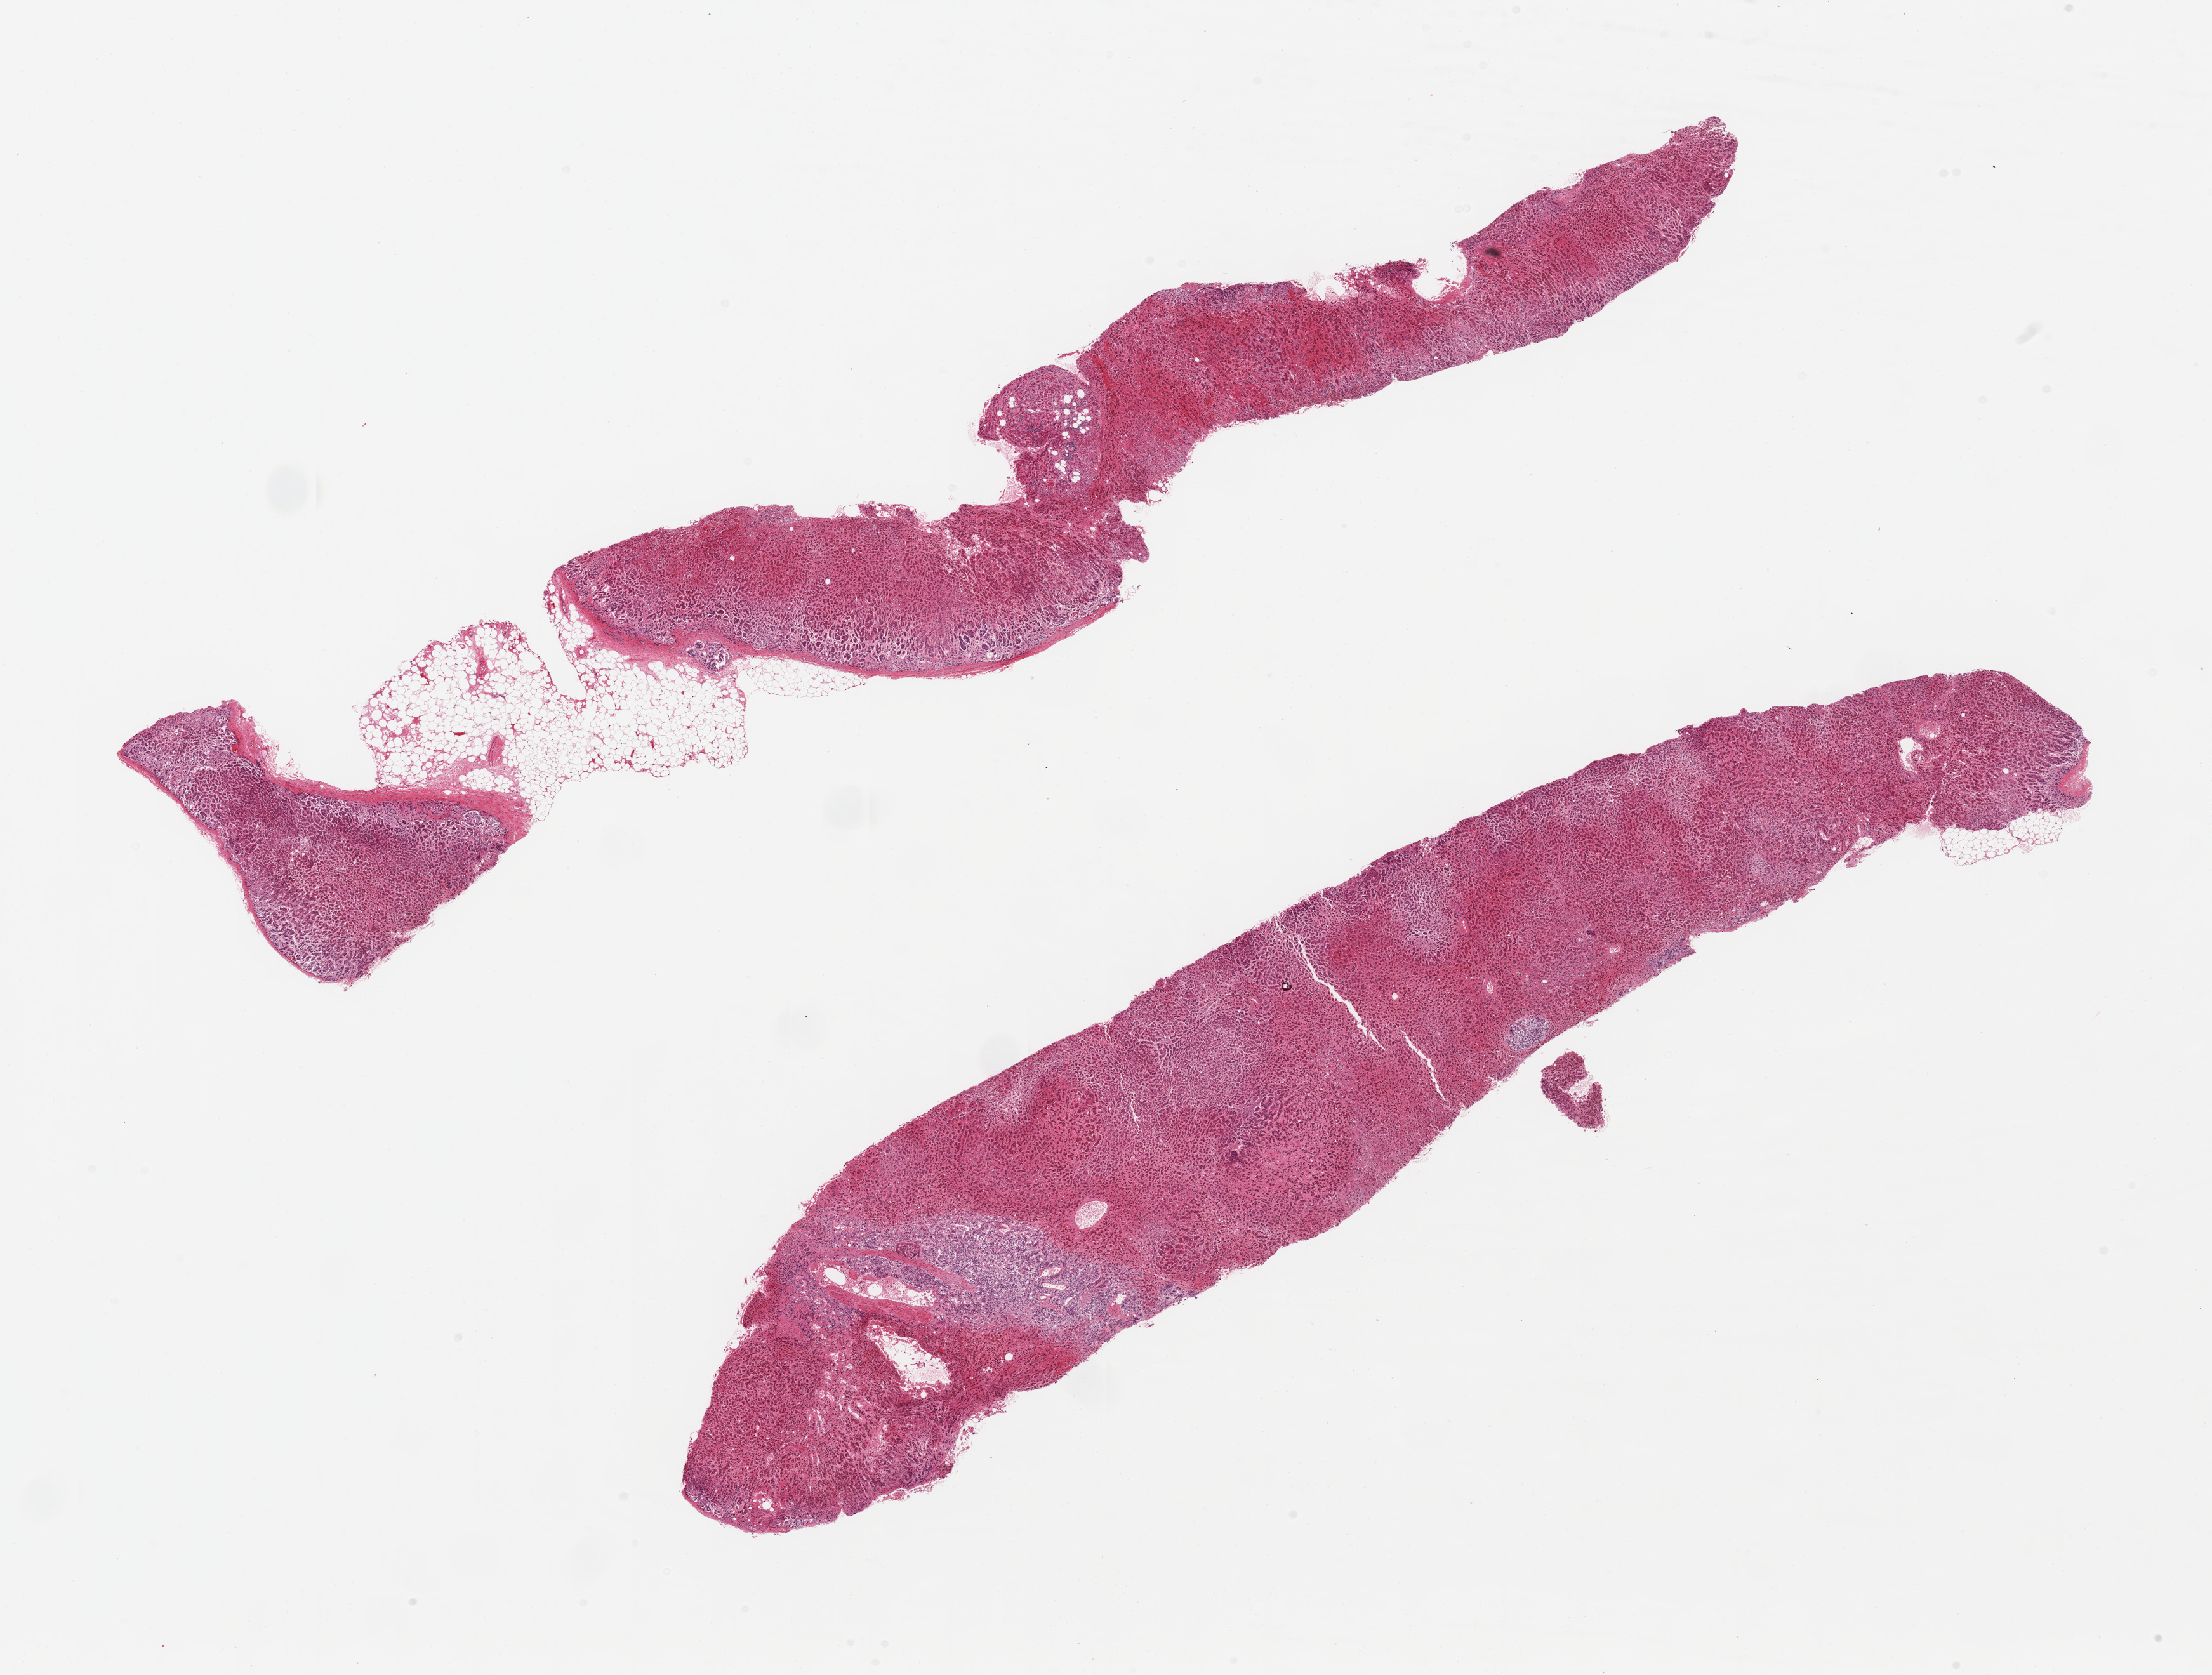
H&E whole-slide image — a low-resolution overview of the entire scanned area, about 27.6 x 20.9 mm (from a 20x scan); PAXgene-fixed, paraffin-embedded tissue; target tissue: adrenal gland; tissue donor sample. Male donor.
Pathologist's review note for this sample: 2 pieces; cortex and medulla.